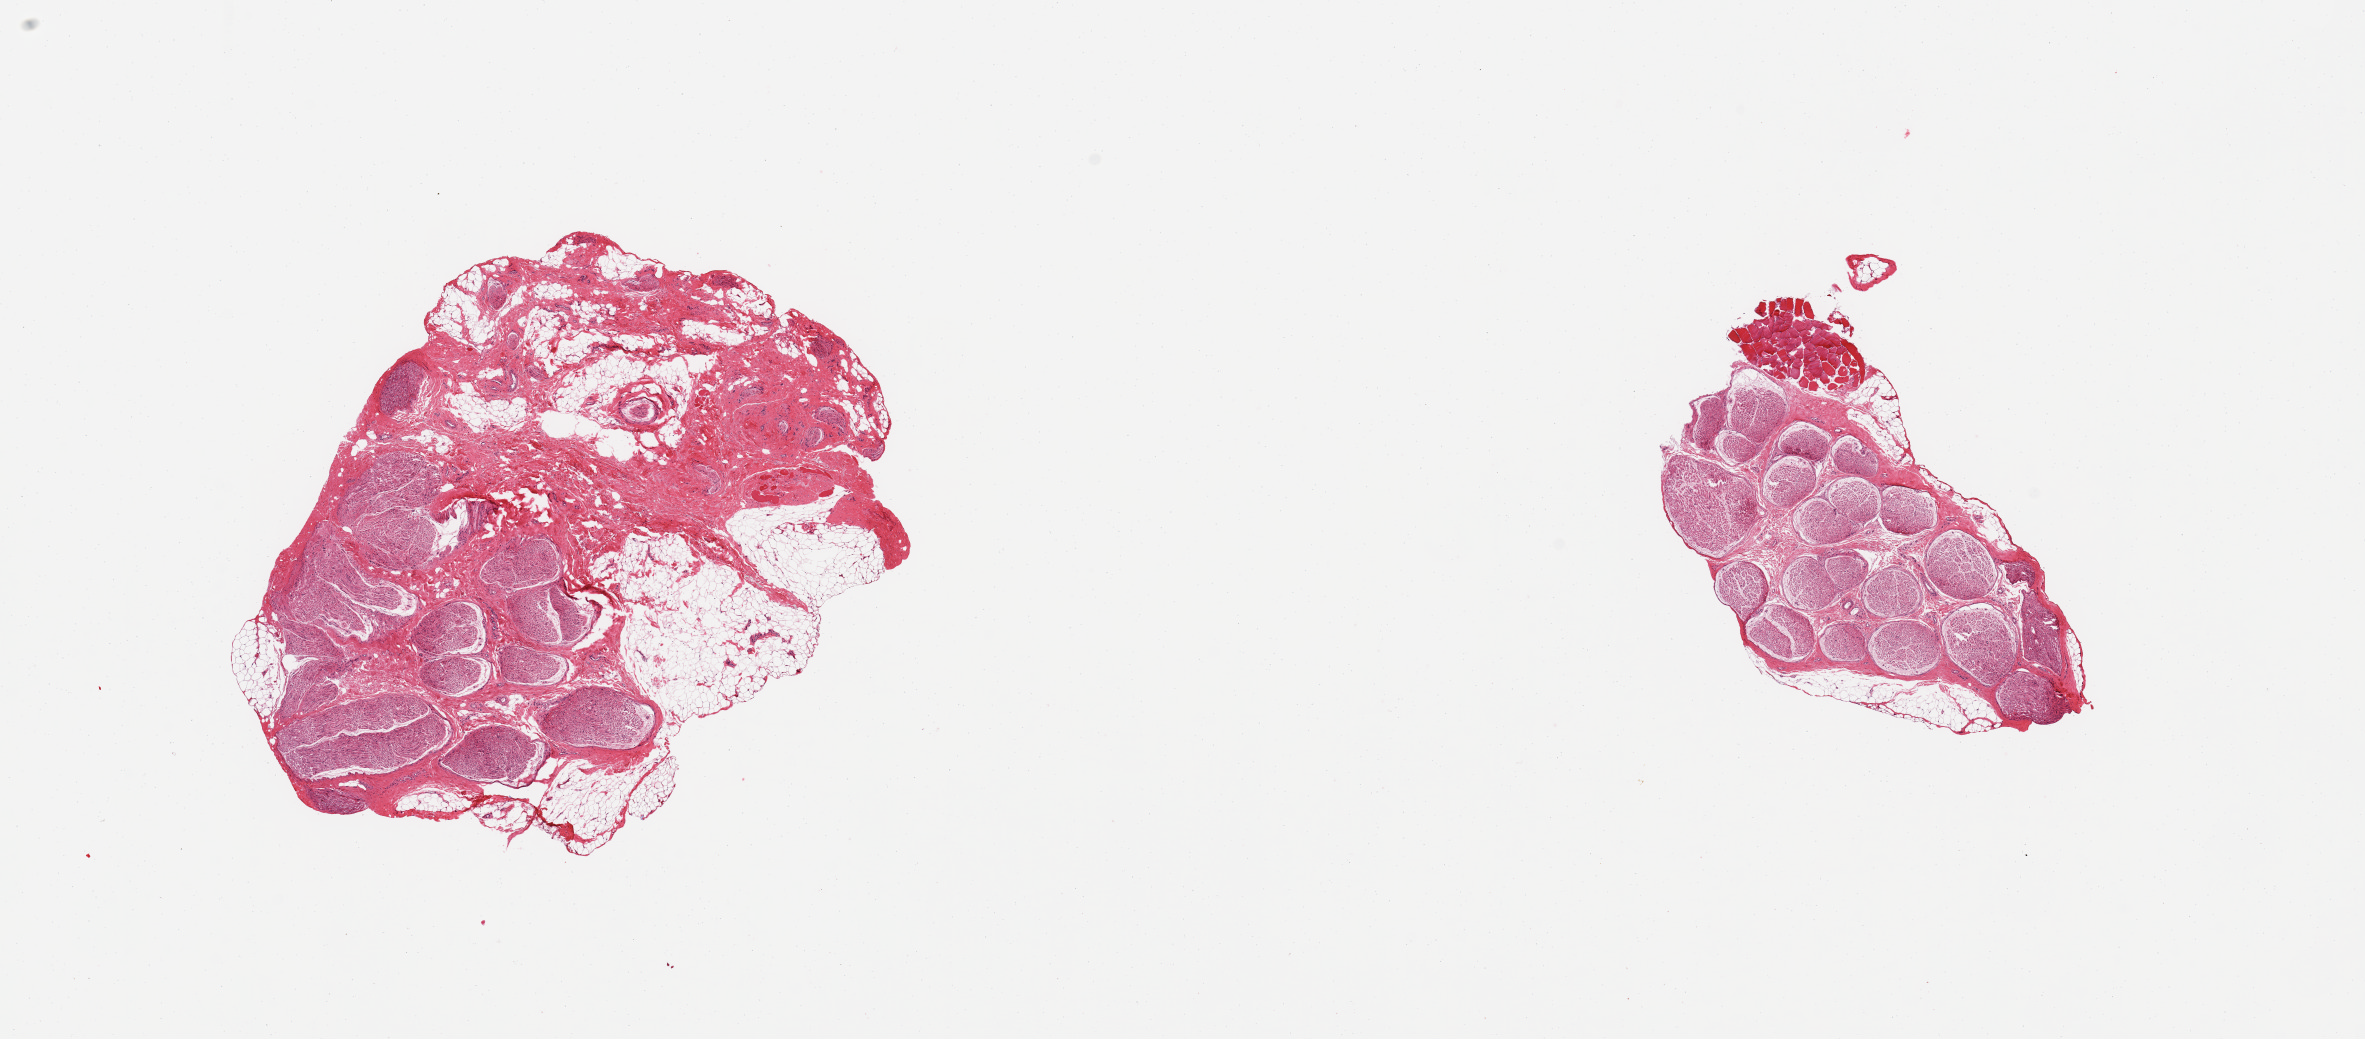
Whole-slide image, haematoxylin and eosin stain, brightfield — whole scanned area (about 18.7 x 8.2 mm, slide scanned at 20x) shown as a low-resolution overview. PAXgene-fixed, paraffin-embedded tissue. Target tissue: tibial nerve. Donor tissue sample.
* review note (as recorded): 2 pieces; 60% external fibrofatty tissue in 1; 10% external muscle & 10% external fat in other piece